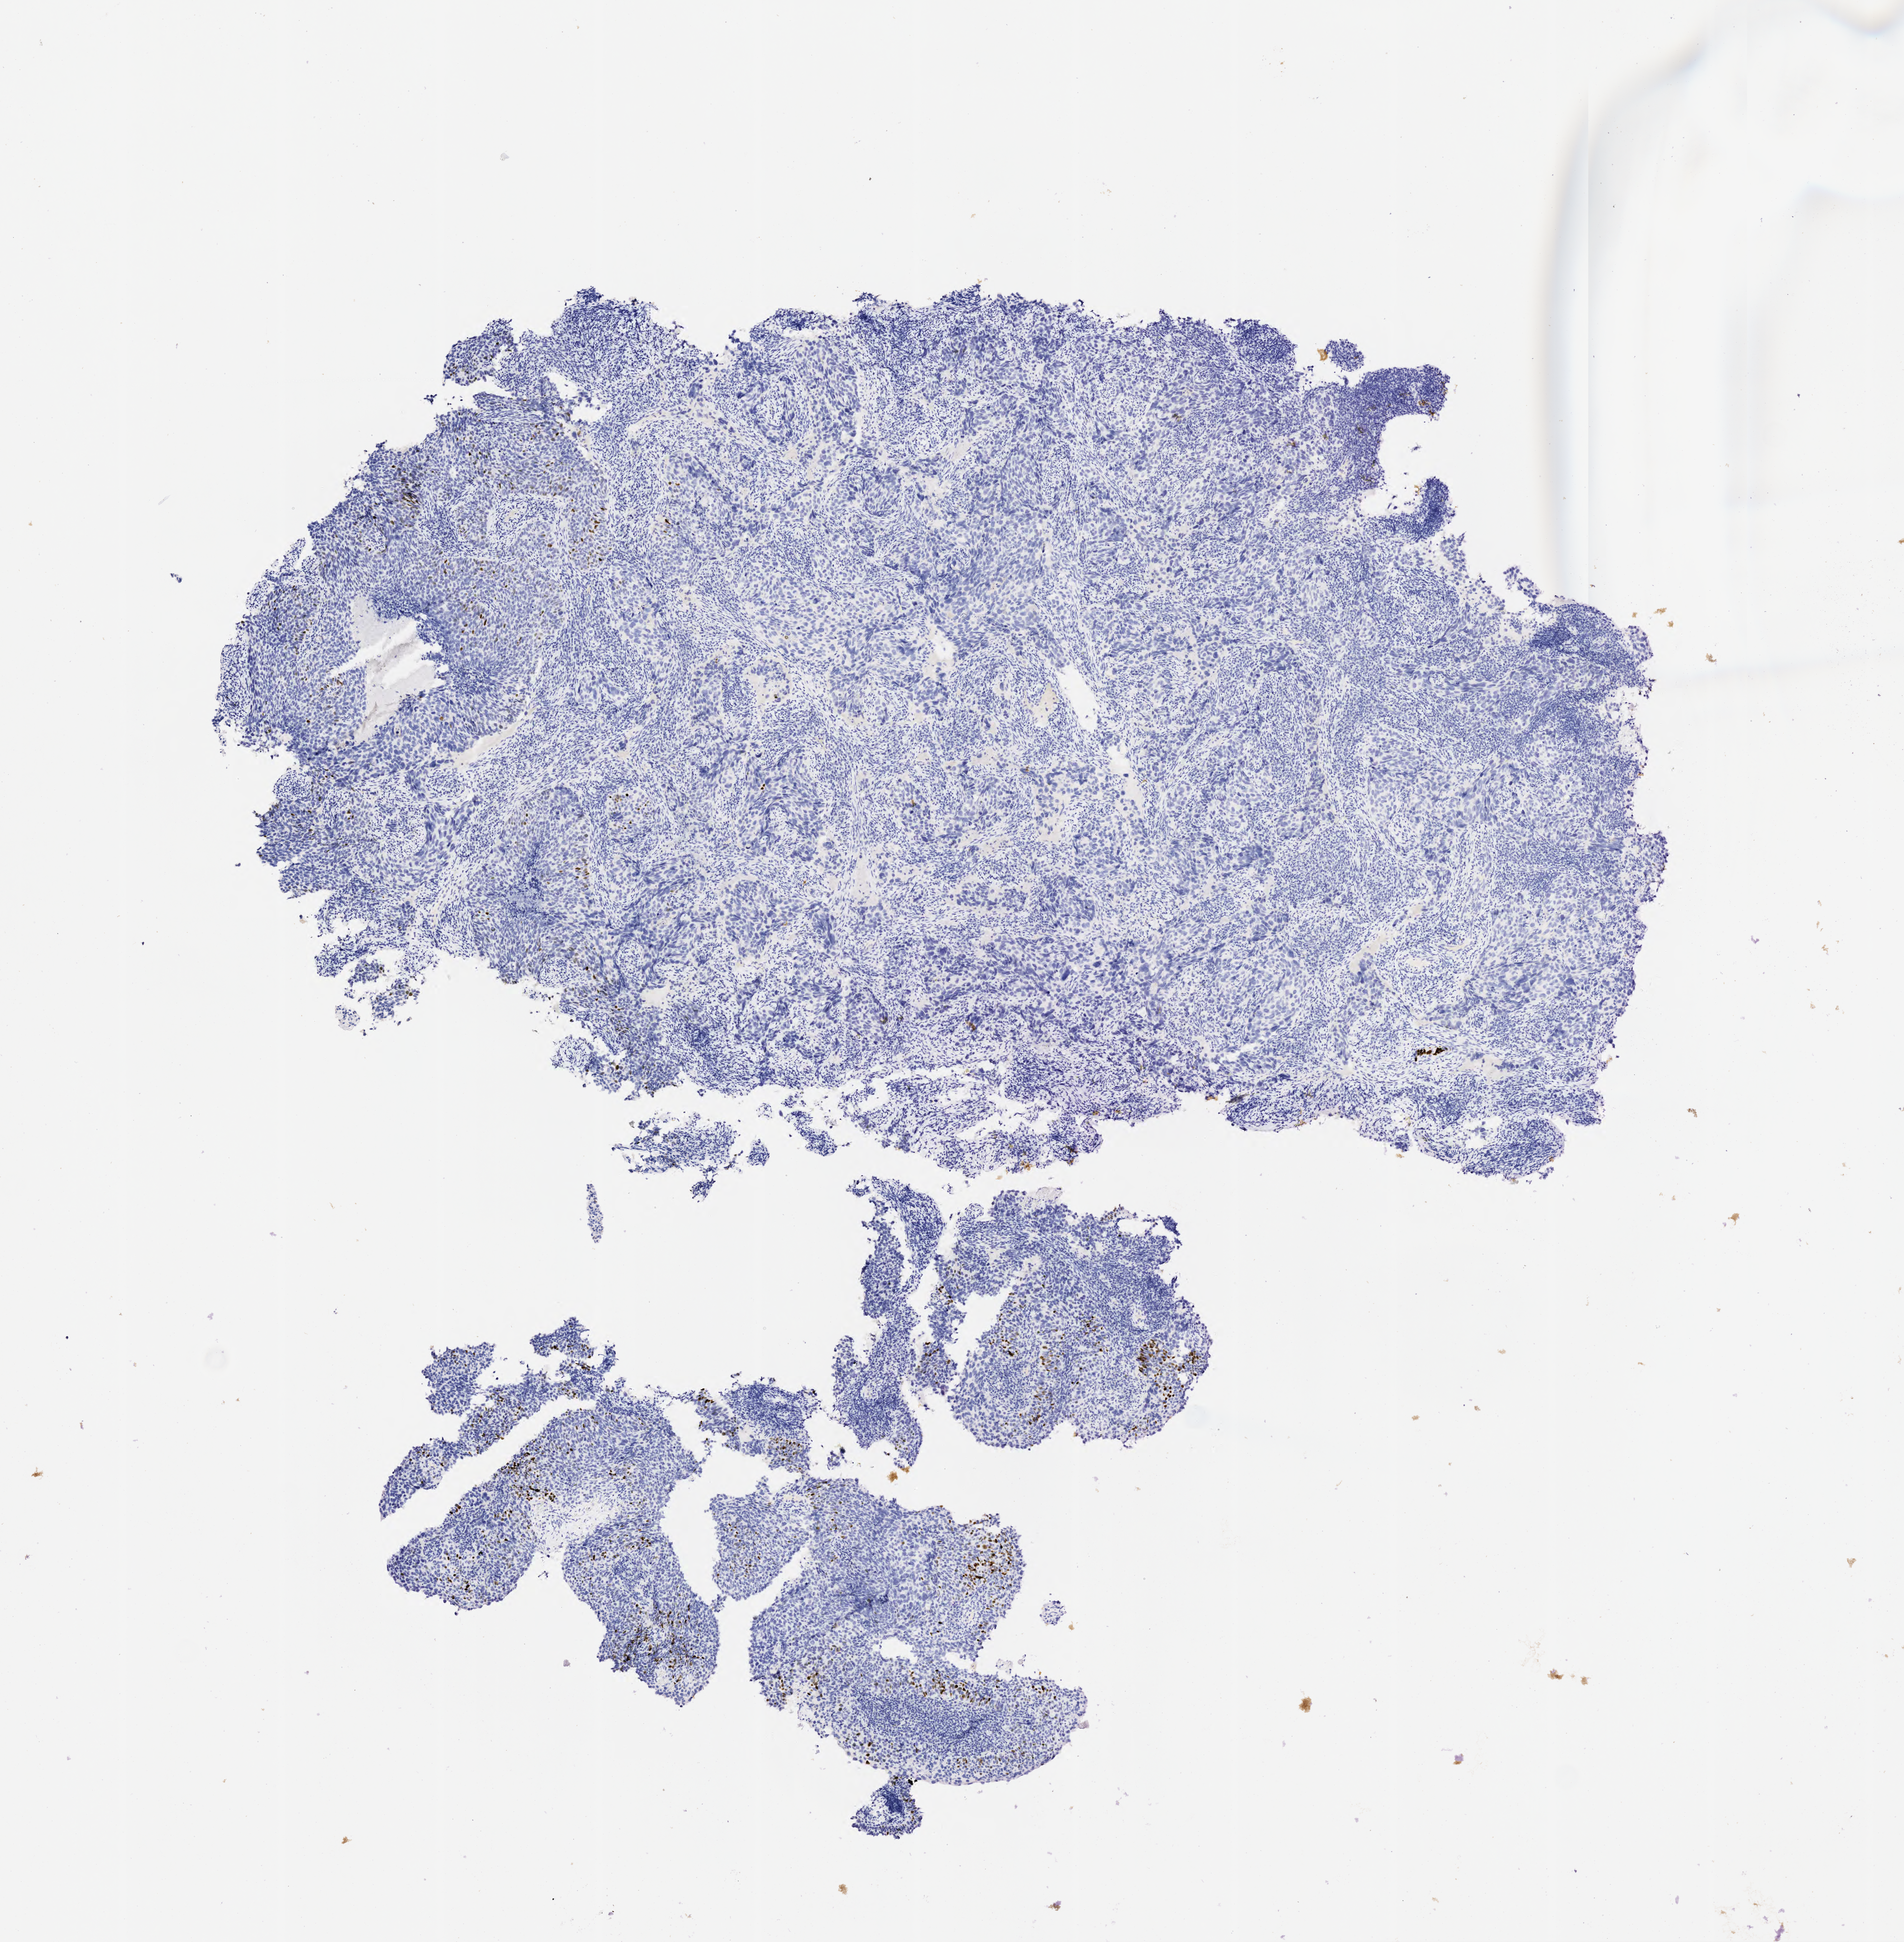
Whole-slide image, immunohistochemical stain for p40 — a low-resolution overview of the entire scanned area, about 6.0 x 6.2 mm; tumor tissue; site: cervix. Patient: female, age 47 years.
* diagnosis: Squamous cell carcinoma, large cell, nonkeratinizing, NOS